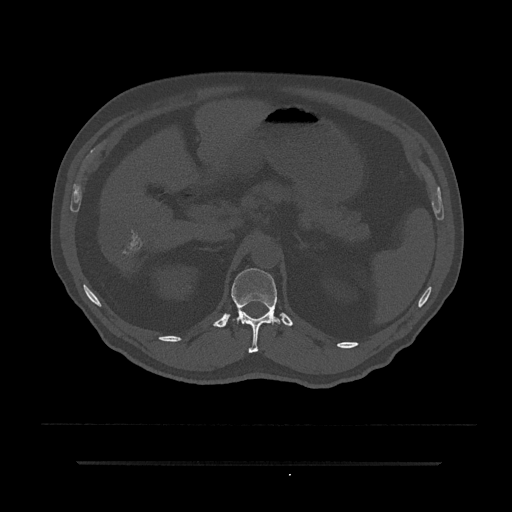
CT including the spine, one axial slice; position 206 of 797 along the scan axis; reconstruction kernel Br40s/3; 120 kVp; bone window (W 1800 / L 400 HU); 0.5 mm slice thickness; 512 × 512 image matrix, field of view 464 × 464 mm. Patient: male, 59 years. Case-level facts recorded for this patient, not image findings: primary cancer: bile ducts; vertebrae with lytic lesions (as recorded): T10.
Outlined on this slice (semi-automatically segmented with operator editing):
- T12 vertebra: bounding box (x1, y1, x2, y2) in pixels: (231, 268, 282, 353)